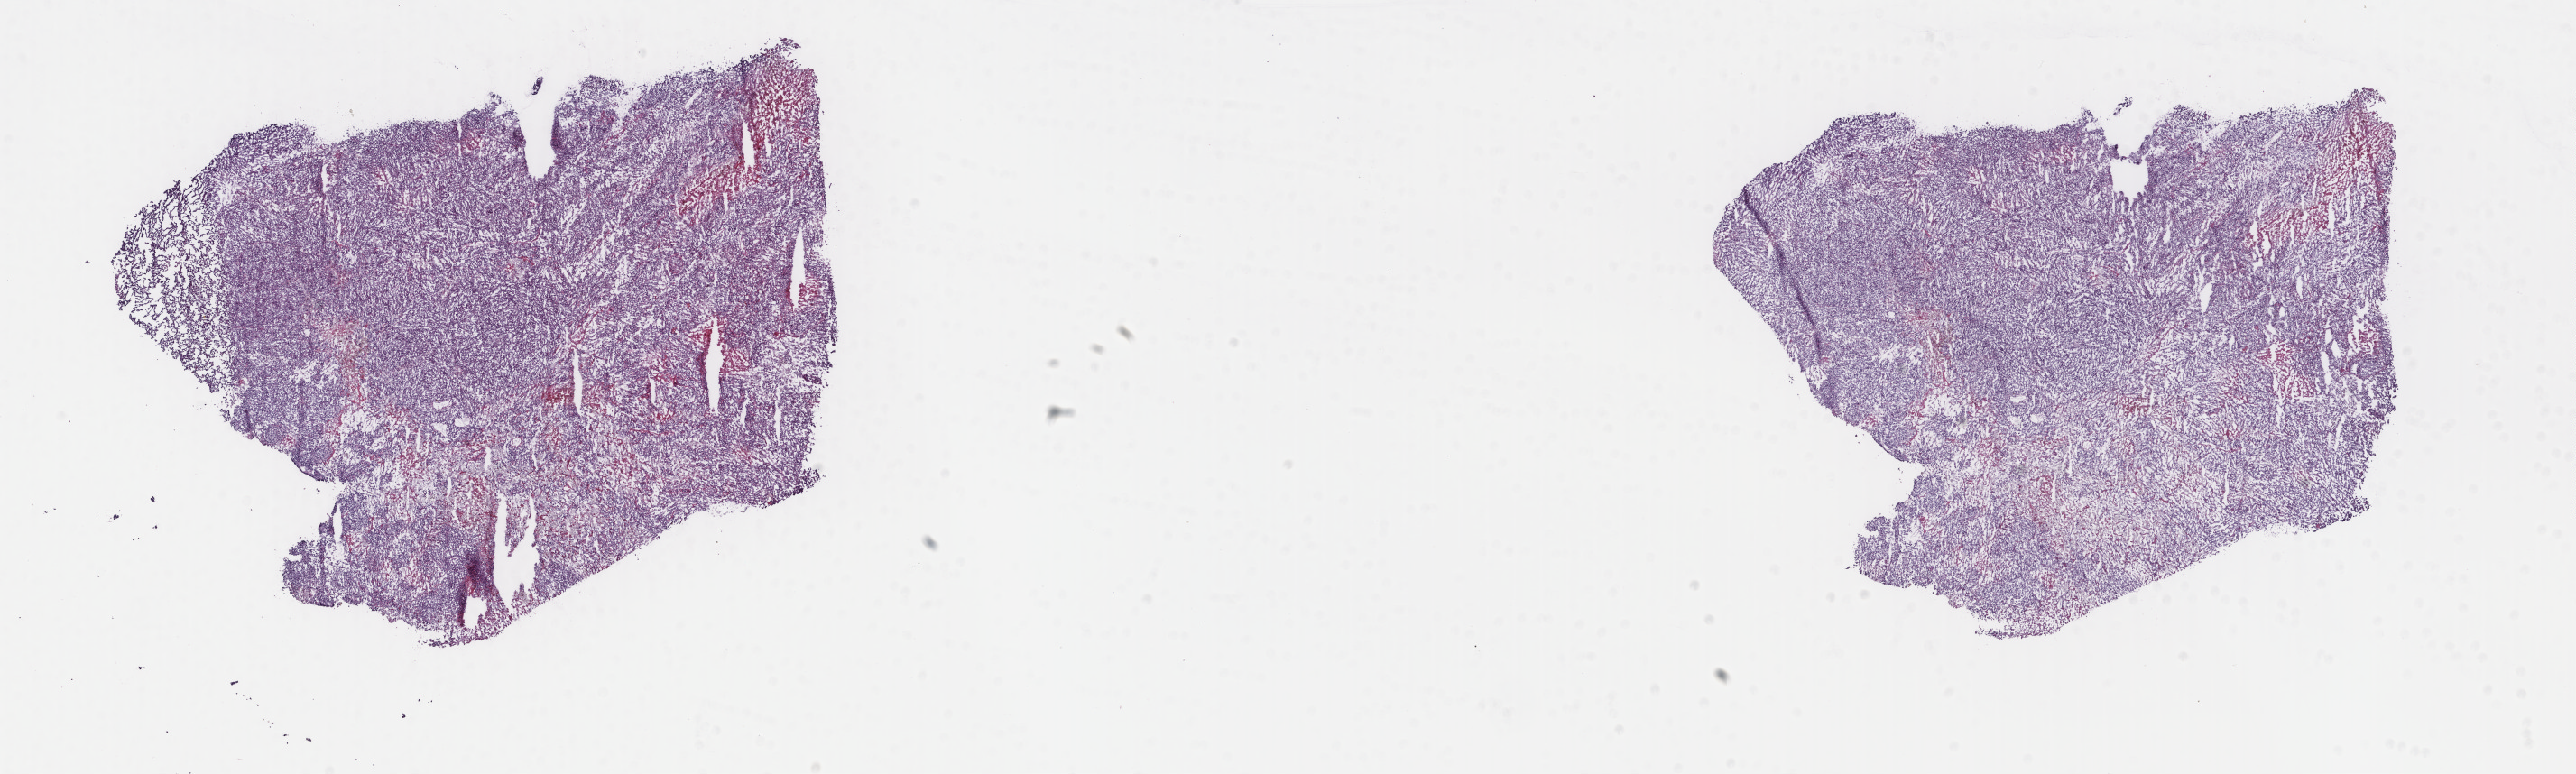
Digitized Hematoxylin and eosin (H&E) stained tissue section (whole slide), low-resolution overview of the scanned area, about 22.7 x 6.8 mm (acquisition: 40x scan), frozen section, metastatic tumour sample, sampled site: skin of trunk. Patient: male, age at initial diagnosis 54 years. Slide review estimates, as recorded: tumour cells 85%, tumour nuclei 85%, normal cells 0%, stromal cells 6%, necrosis 9%. Inflammatory infiltration, as recorded: lymphocyte infiltration 1%, monocyte infiltration 1%, neutrophil infiltration 0%.
This section: metastatic tumour tissue. Patient diagnosis: Malignant melanoma, NOS.